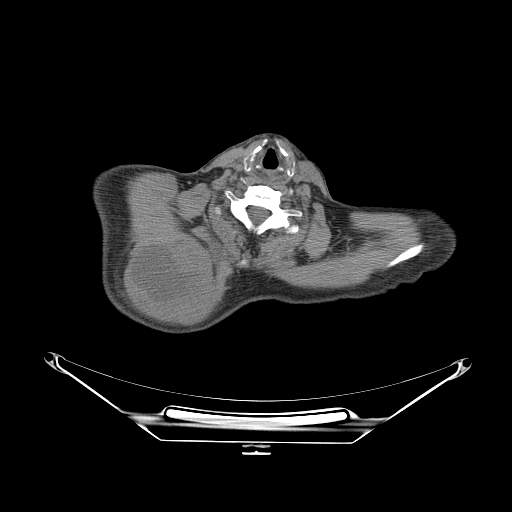
CT of an extremity soft-tissue mass (from a PET/CT study), one axial slice; slice 215 of 267 in the series (ordered by position); reconstruction kernel STANDARD; soft-tissue window (W 400 / L 40 HU); 512 × 512 image matrix, field of view 500 × 500 mm. Male patient. Case-level facts recorded for this patient, not image findings: histological type: pleiomorphic spindle cell undifferentiated; grade: high; site of the primary tumour: right parascapusular.
Outlined on this slice (expert contour drawn on MRI and transferred to this co-registered scan by the dataset authors):
- gross tumour volume including surrounding oedema: box from (x=121, y=238) to (x=232, y=318) px
- gross tumour volume (mass): (x=130, y=244)–(x=209, y=316)